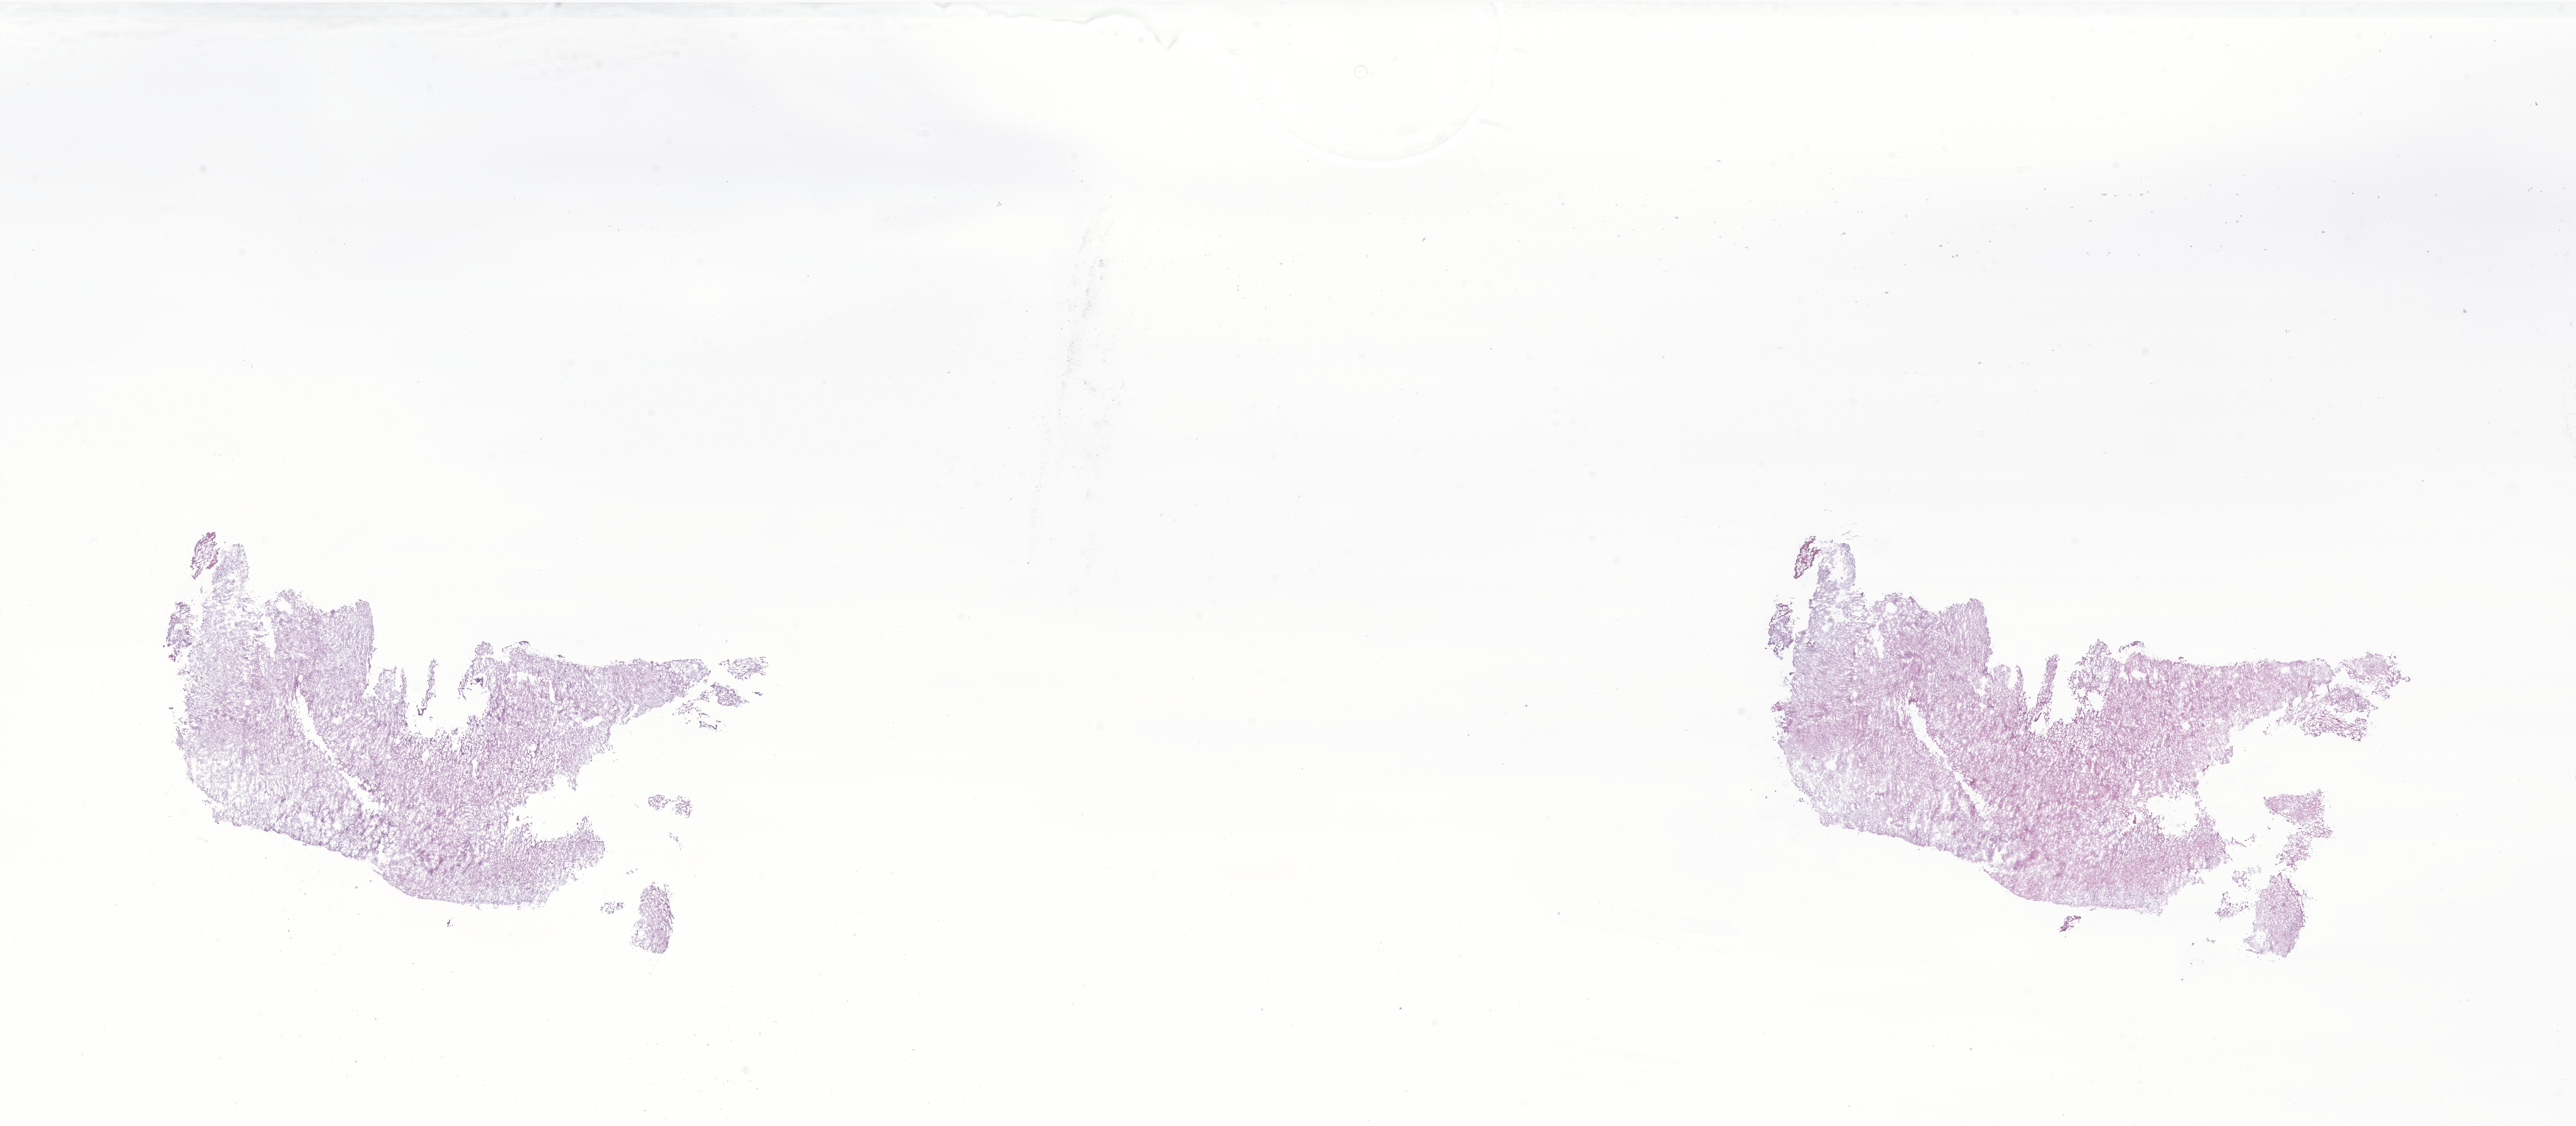
H&E whole-slide image of tumor tissue from the brain — a low-resolution overview of the entire scanned area, about 29.7 x 13.0 mm, frozen section (OCT-embedded). Patient male; age 166 months (13 years 10 months).
Diagnosis (ICD-O-3 morphology term): Ganglioglioma, NOS.